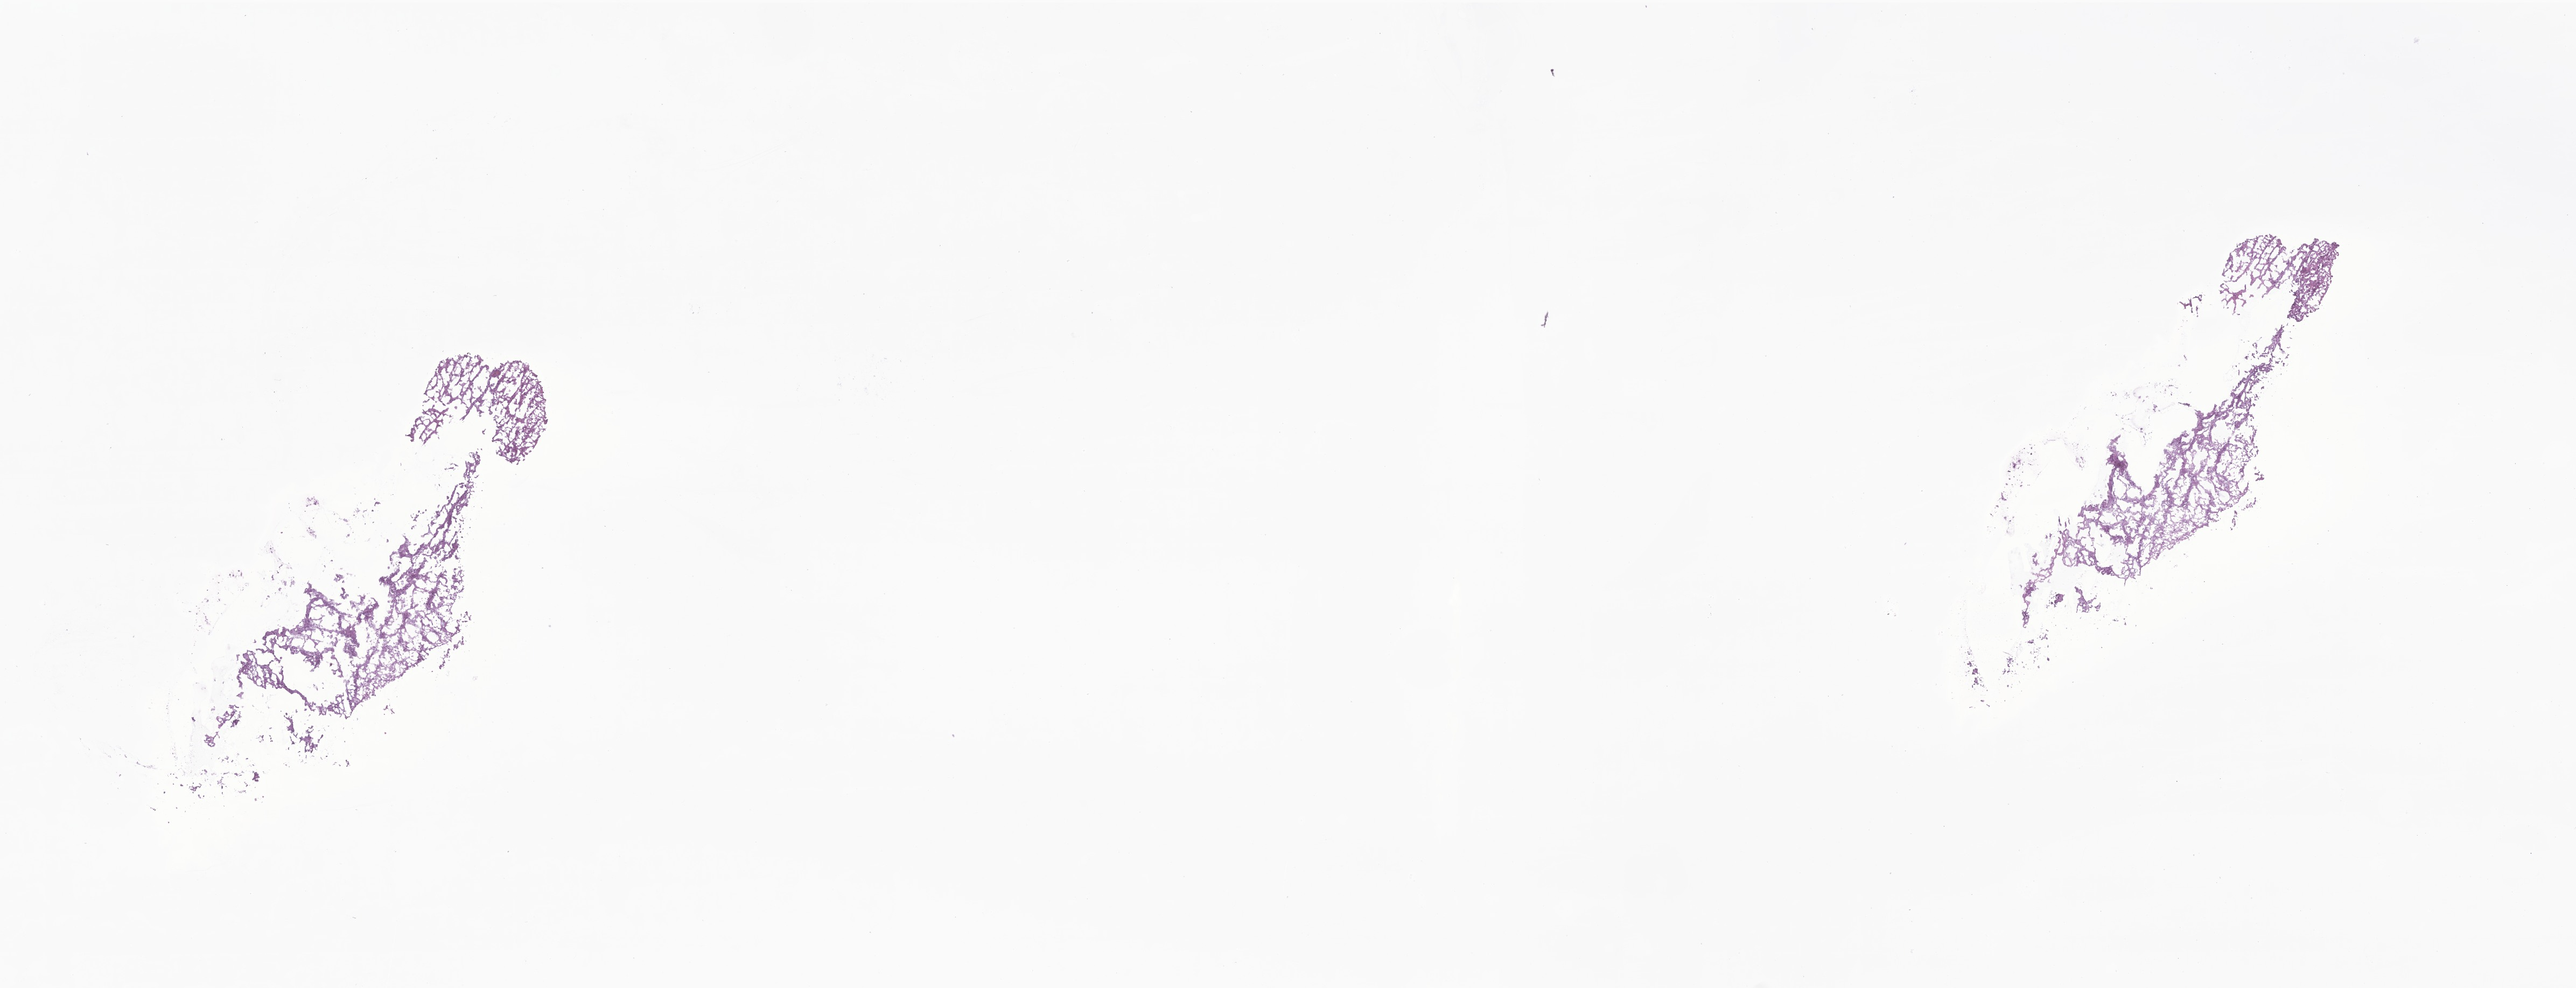
Digitized haematoxylin and eosin-stained section of tumor tissue from the parietal lobe — a low-resolution overview of the entire scanned area, about 20.2 x 7.7 mm. Frozen section. Male patient, age 122 months (10 years 2 months).
Diagnosis (ICD-O-3 morphology term): Glioma, malignant.